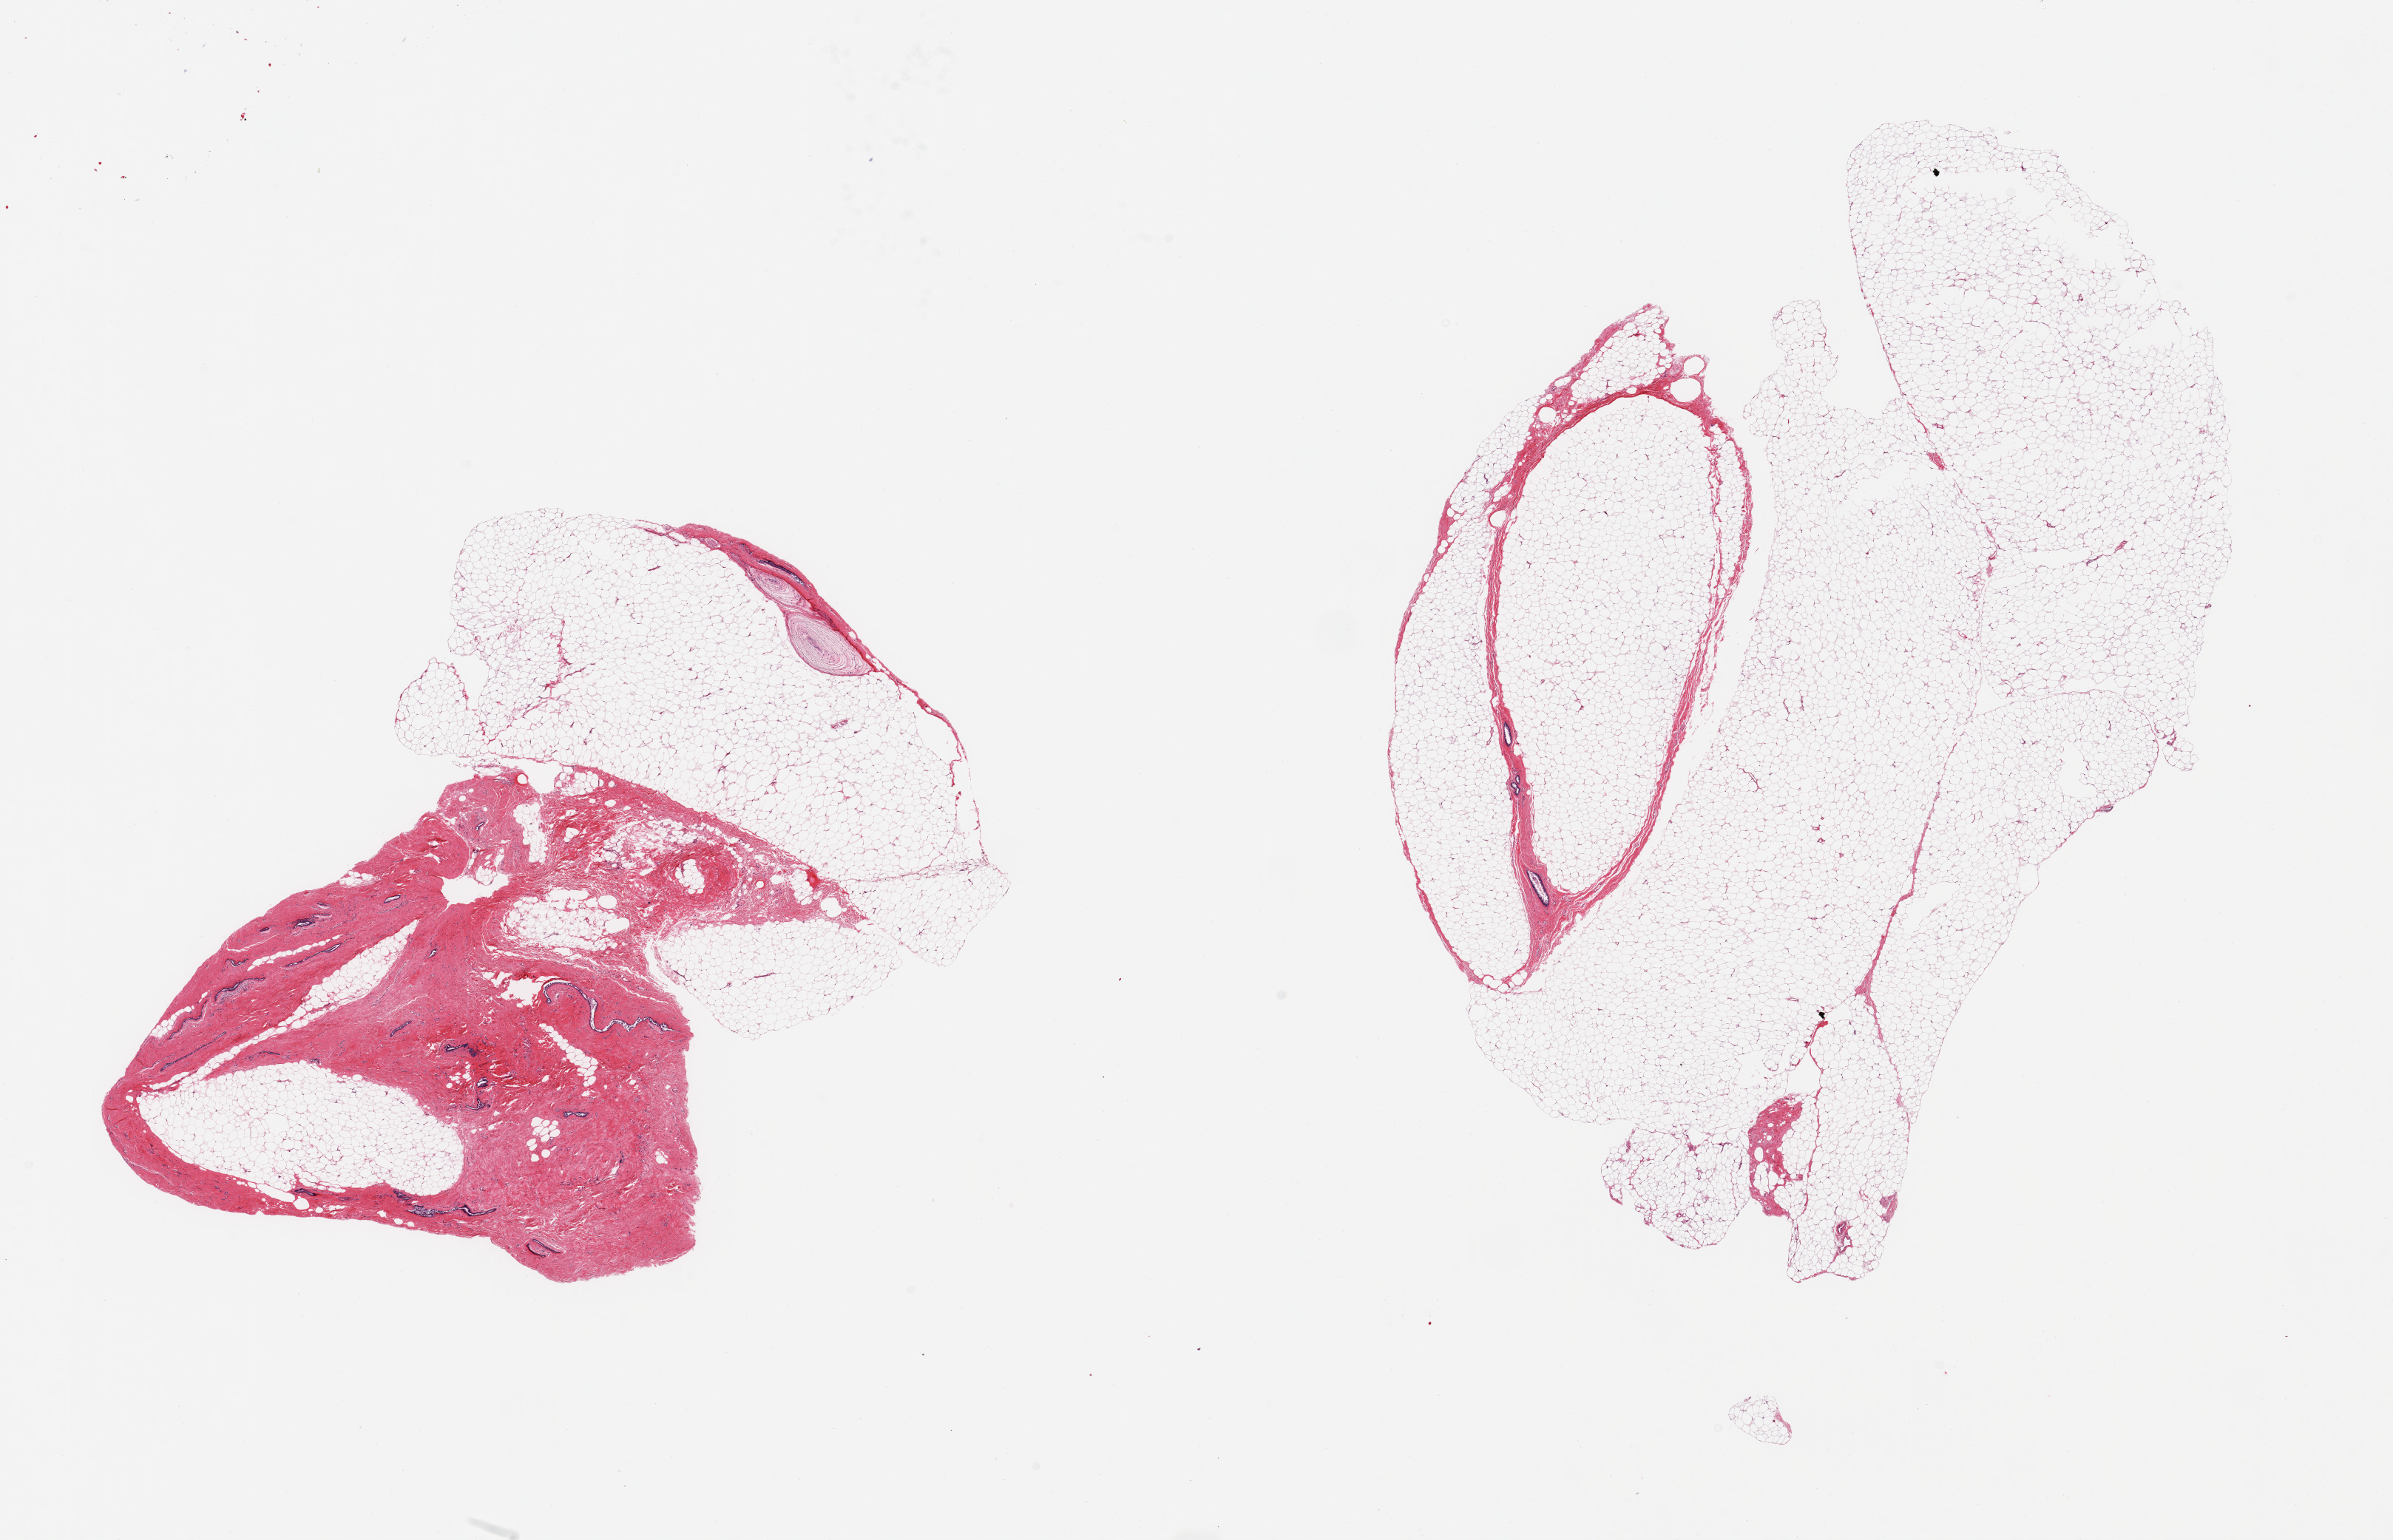
Digitized H&E-stained section, a low-resolution overview of the entire scanned area, about 25.6 x 16.5 mm, PAXgene-fixed, paraffin-embedded tissue, target tissue: breast, donor tissue sample. Male donor.
• reviewer comment on this tissue sample: 2 pieces, gynecomastoid stromal and ductal hyperplasia